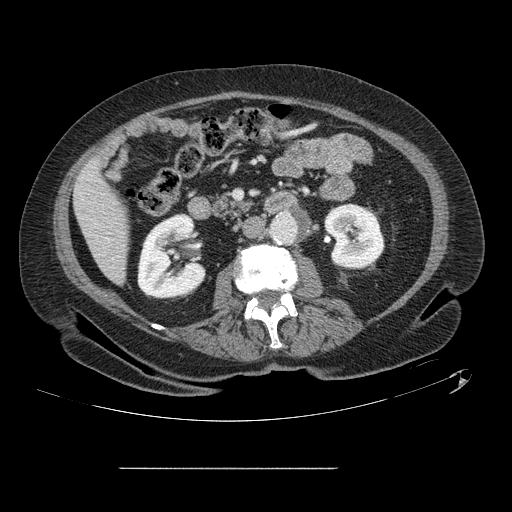
Contrast-enhanced abdominal CT, one axial slice. Position 32 of 148 along the scan axis. 120 kVp. Intravenous contrast given. Soft-tissue window (W 400 / L 40 HU). 2.5 mm slice thickness. 512 × 512 image matrix, field of view 439 × 439 mm. Female patient, age 75 years. From the clinical record (not read from this slice): diagnosis: colorectal cancer liver metastases, imaged before liver resection; multiple liver metastases: no; largest metastasis: 2.4 cm; chemotherapy before resection: no.
Structures marked on this image (manually delineated by an expert):
- liver: bounding box [x1, y1, x2, y2] px = [75, 162, 128, 283]
- planned liver remnant (the part of the liver to remain after resection): [75, 162, 128, 282]